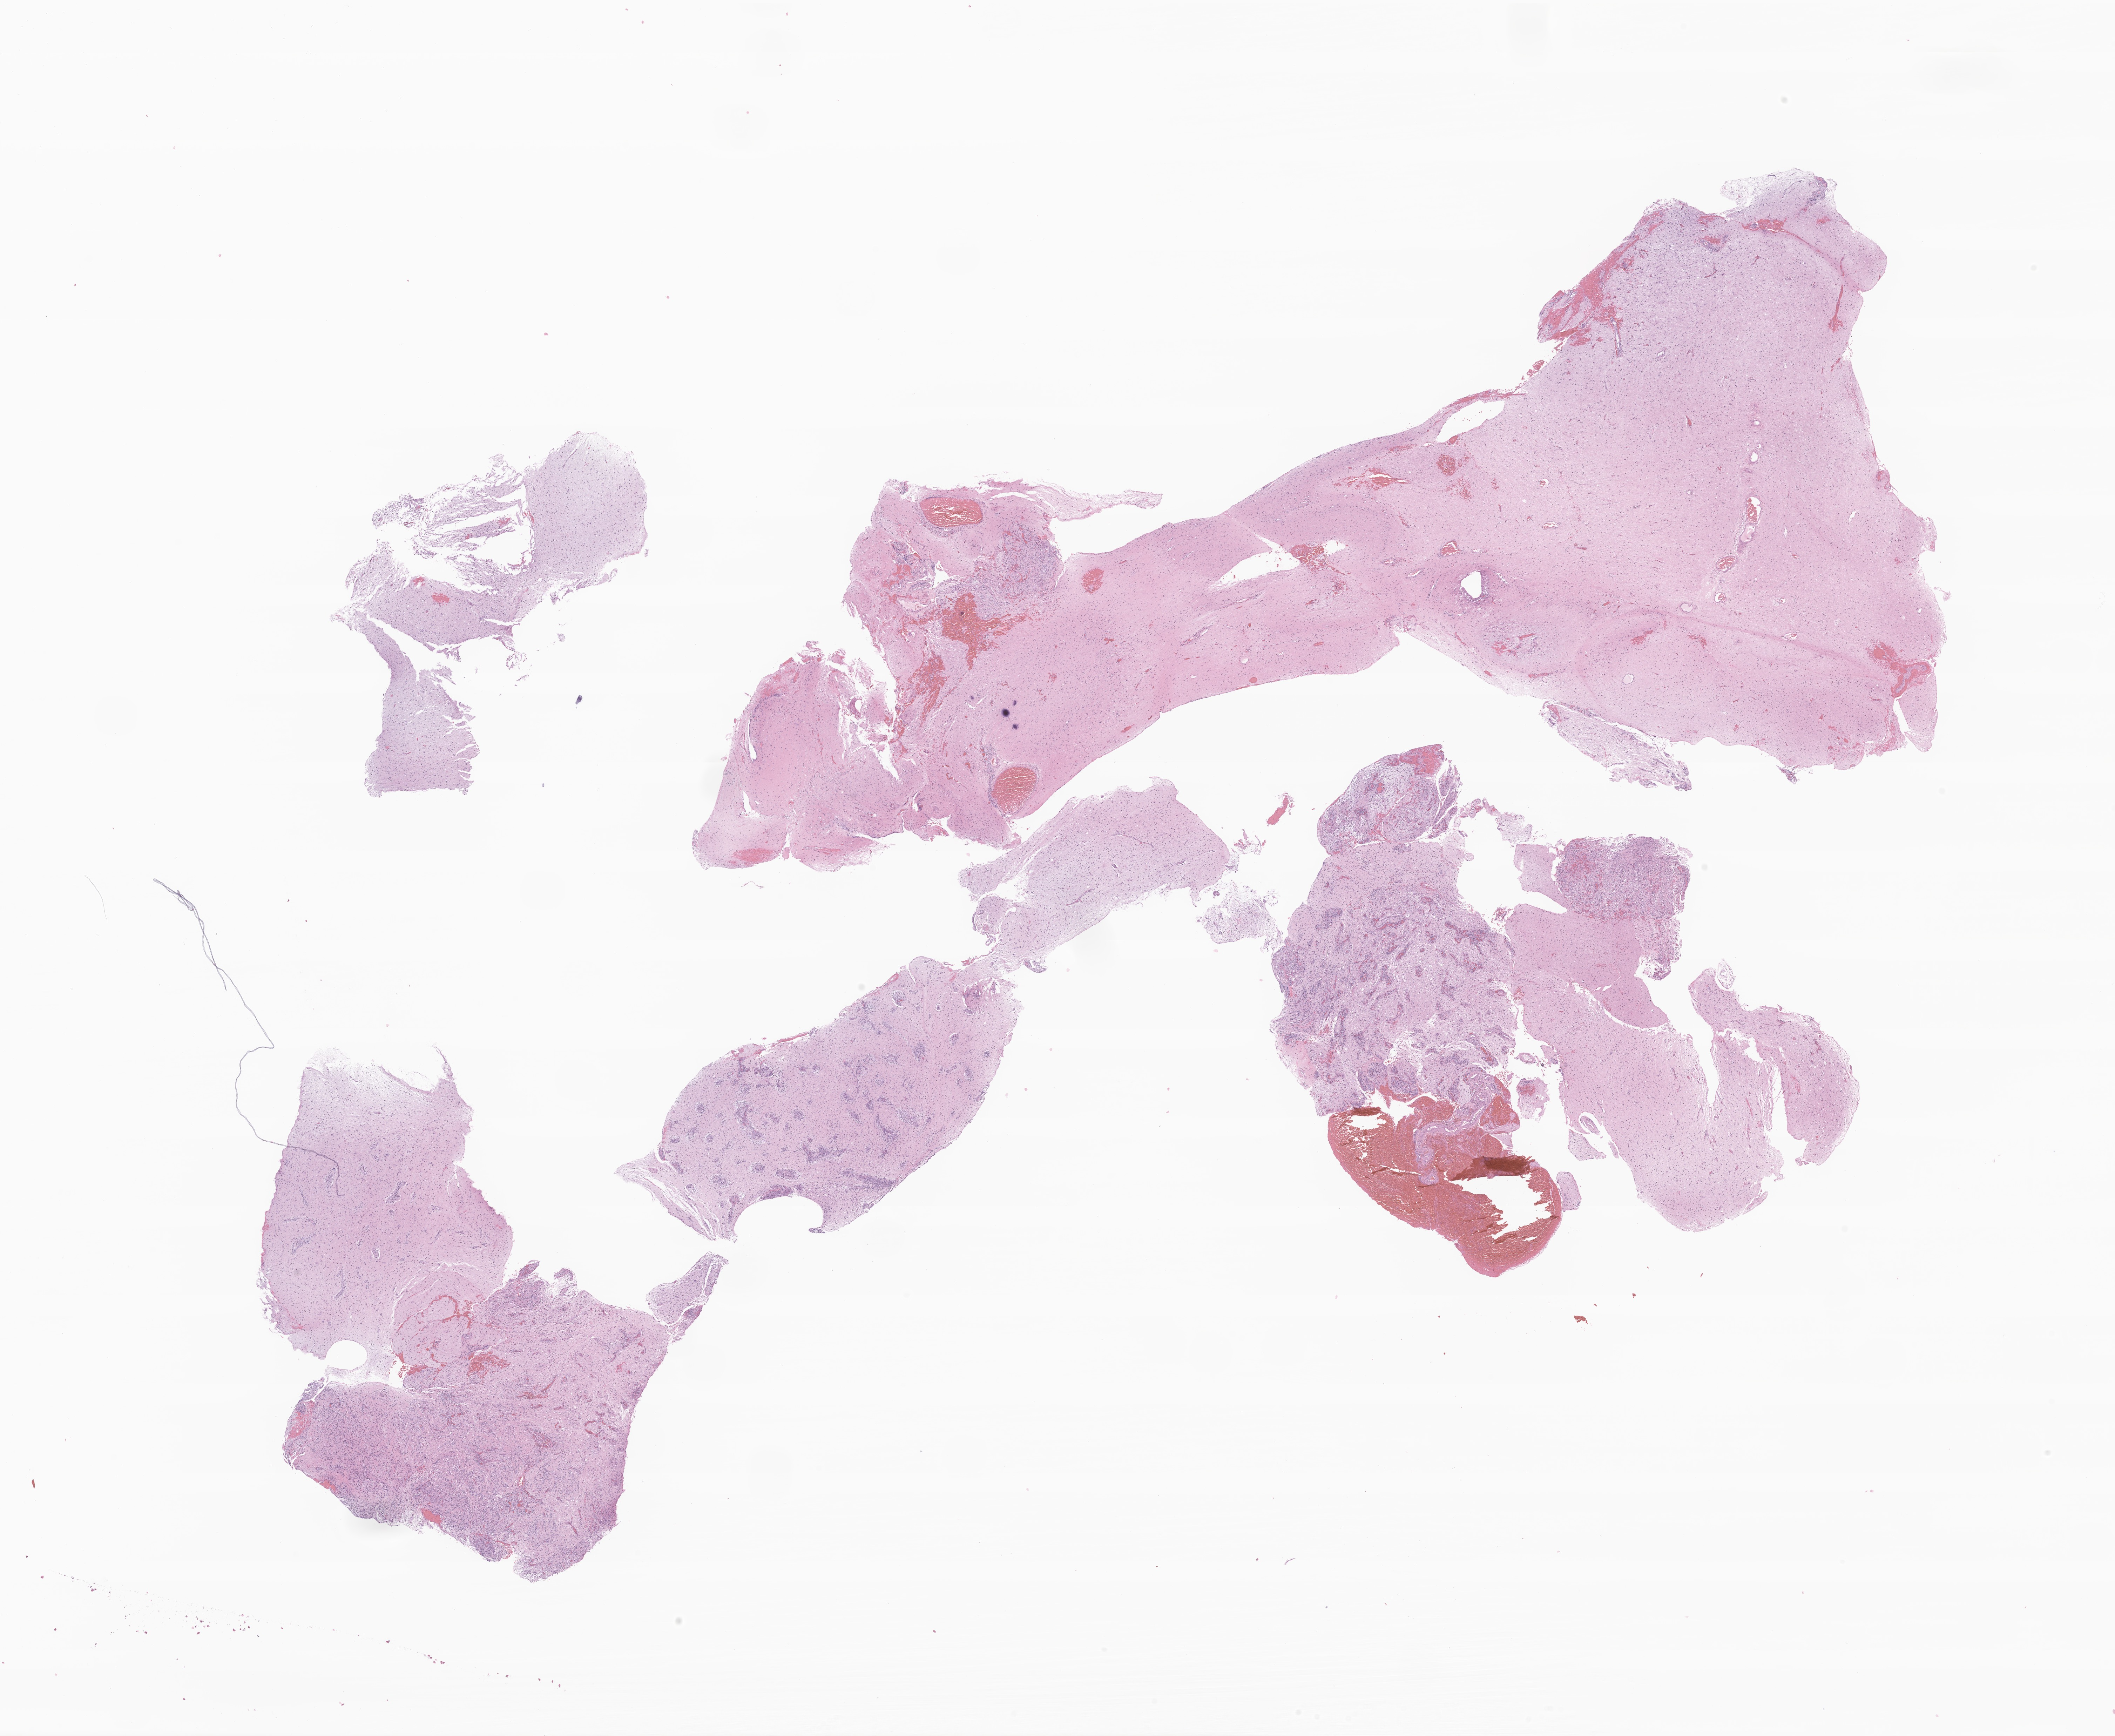
H&E whole-slide image of tumor tissue from the brain, a low-resolution overview of the entire scanned area, about 25.4 x 20.9 mm; formalin-fixed paraffin-embedded section. Patient male; age 201 months (16 years 9 months).
* diagnosis (ICD-O-3 morphology term): Neoplasm, uncertain whether benign or malignant